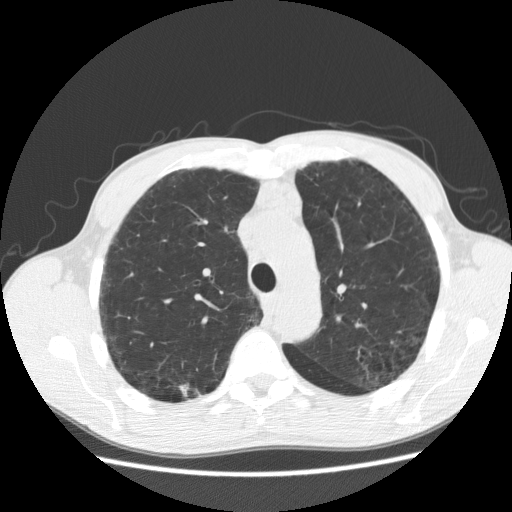
Low-dose screening chest CT, axial slice, second screening round (one year after baseline), lung window (W 1500 / L -600 HU), 2.5 mm slice thickness, standard (soft-tissue) reconstruction kernel (STANDARD). Male participant, aged 60 years at enrolment. Current smoker at enrolment.
- Lesion marked by an expert reader, box from (x=170, y=377) to (x=211, y=409) px.
- Reader record for this screening exam (exam-level; its link to the box is not recorded): non-calcified nodule or mass ≥4 mm, right upper lobe, 8 × 5 mm, poorly defined margins, soft tissue attenuation, pre-existing on the prior screen: yes; interval growth: yes.
- Later outcome: lung cancer diagnosed 204 days after this screen — squamous cell carcinoma, NOS, right upper lobe, well differentiated (G1), stage IA (AJCC 6th edition), 15 mm at pathology.